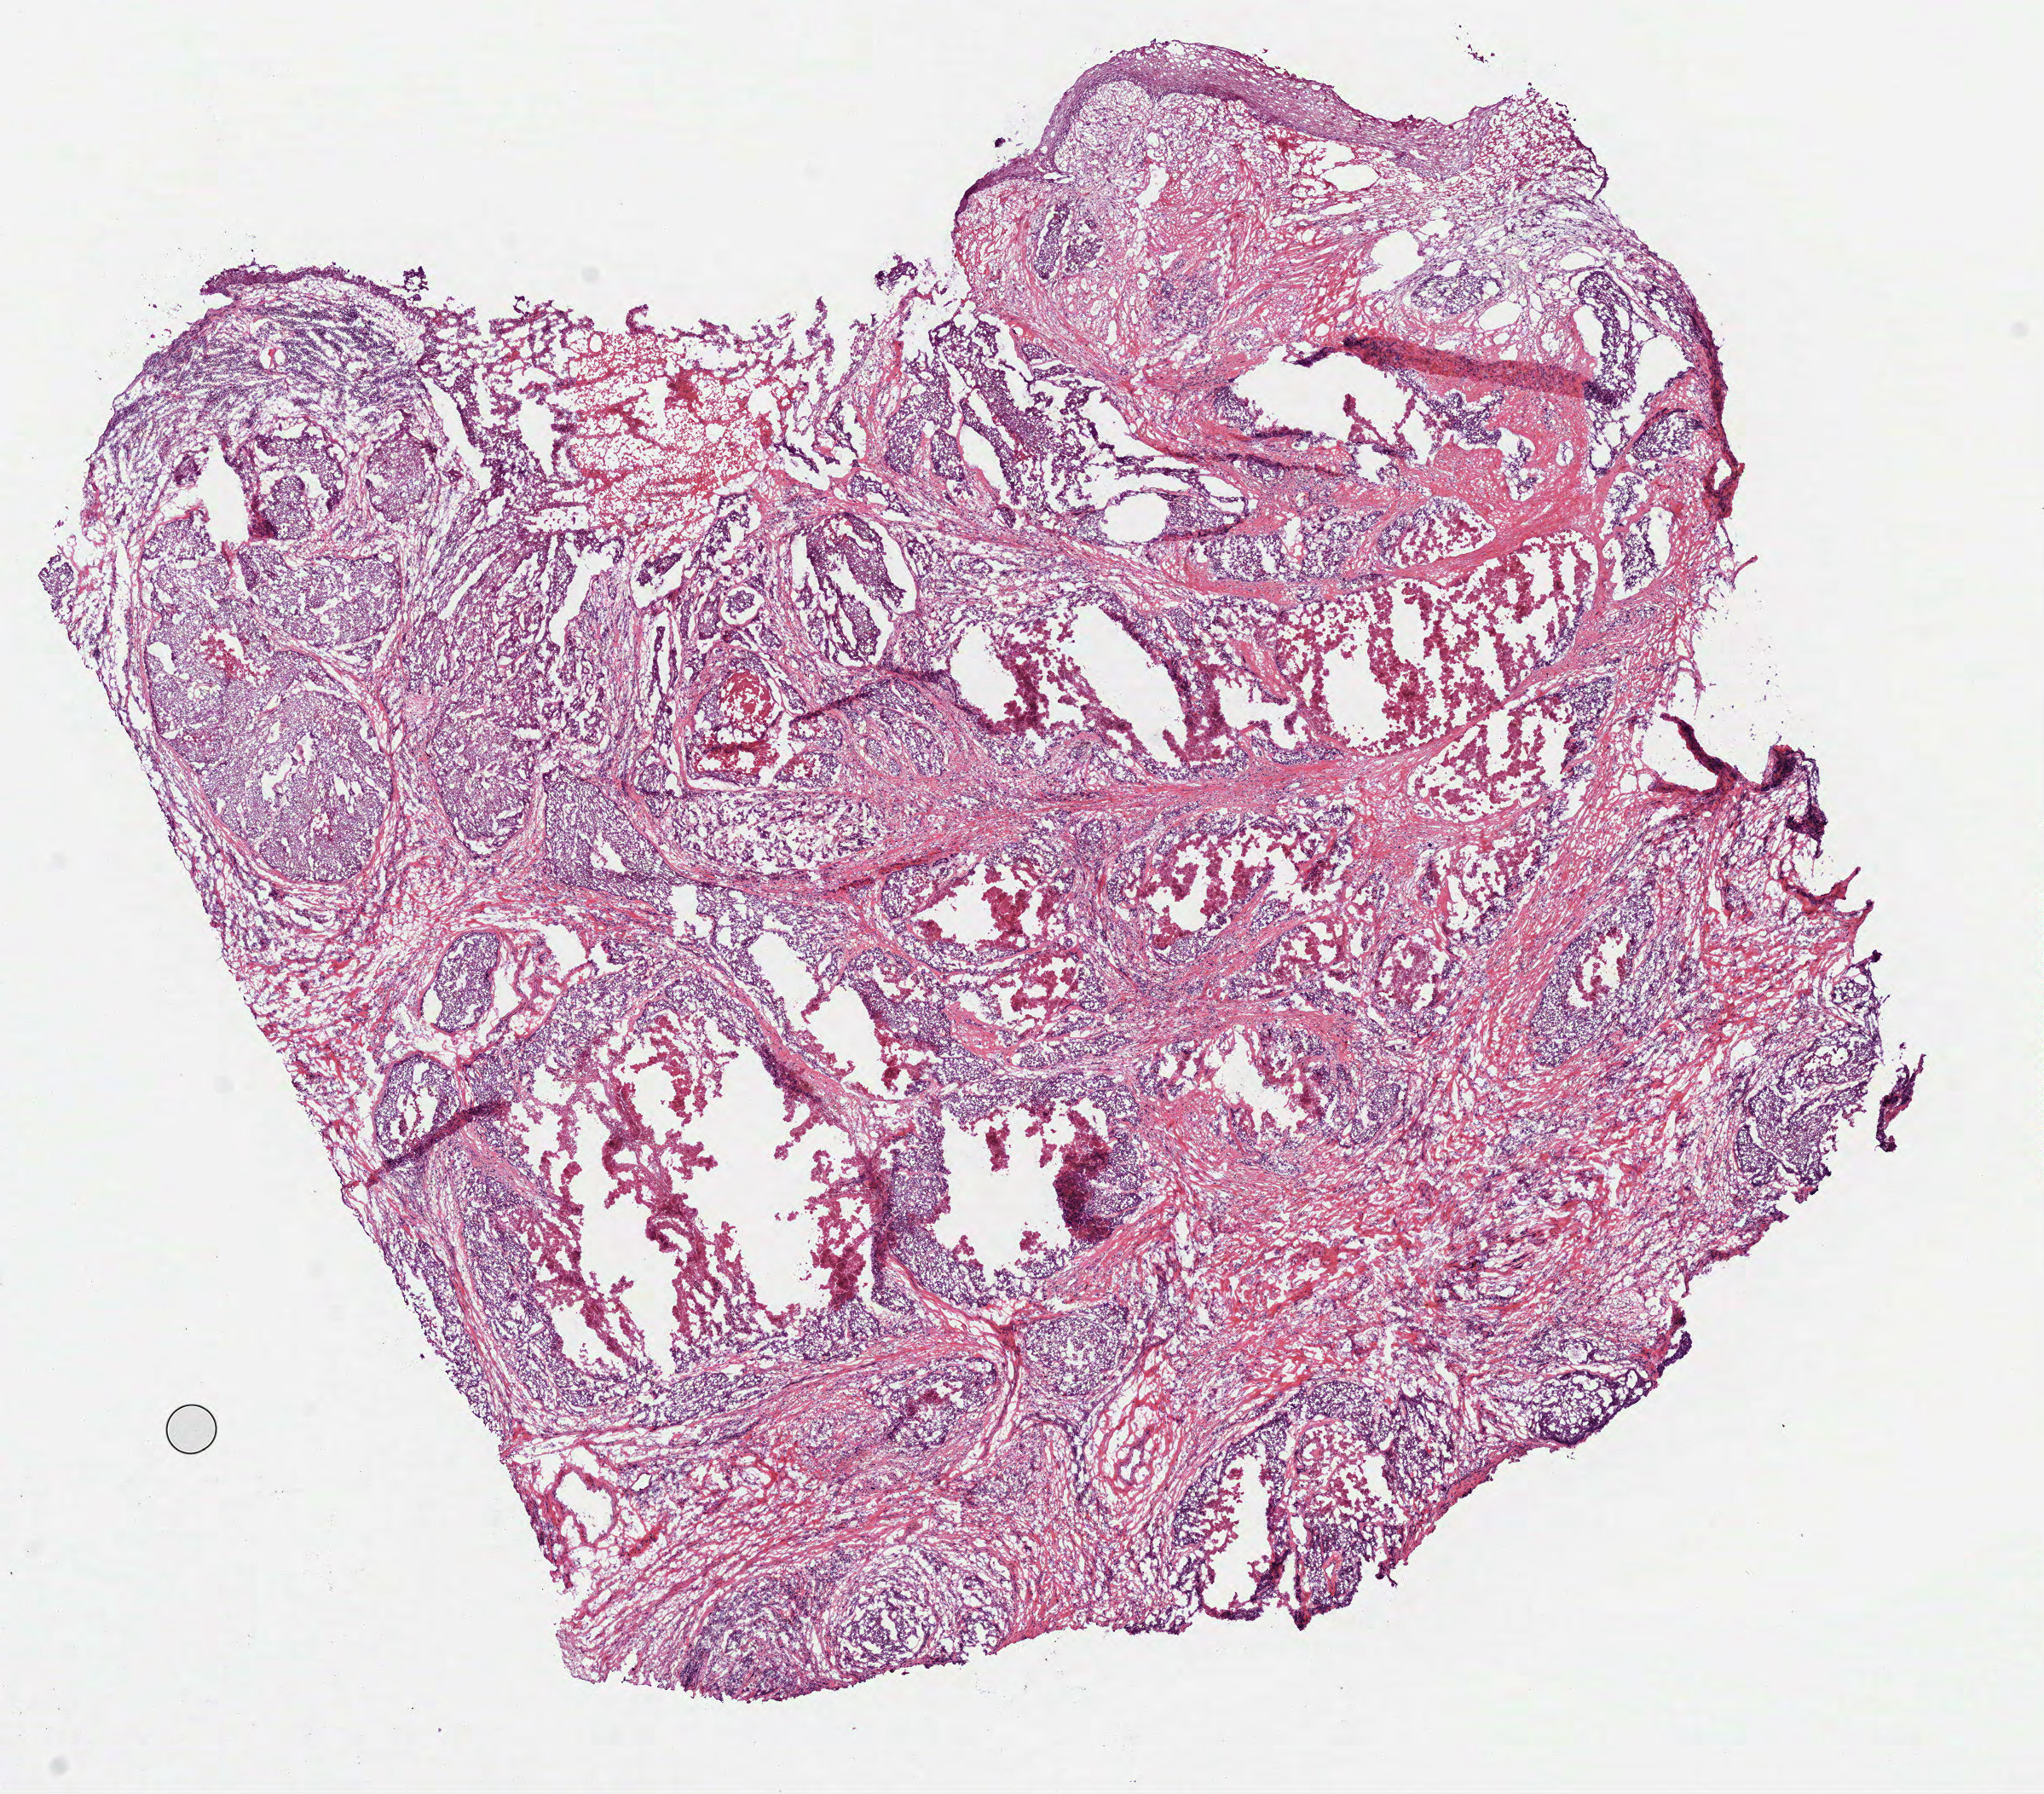
Whole-slide histology image, Hematoxylin and eosin (H&E) stained, a low-resolution overview of the entire scanned area, about 9.7 x 8.5 mm (from a 40x scan). Frozen section from the top of the tissue portion. Head and neck, primary tumour sample. Patient: male, age at initial diagnosis 65 years. Histologic grade: G2 (moderately differentiated). Pathologist review of this section (percent, as recorded): tumour cells 70%, tumour nuclei 71%, normal cells 0%, stromal cells 10%, necrosis 20%. Inflammatory infiltration, as recorded: lymphocyte infiltration 17%, monocyte infiltration 1%, neutrophil infiltration 2%.
• TNM: T4a NX
• pathologic diagnosis: Squamous cell carcinoma, NOS
• AJCC pathologic stage: IVA (7th edition)